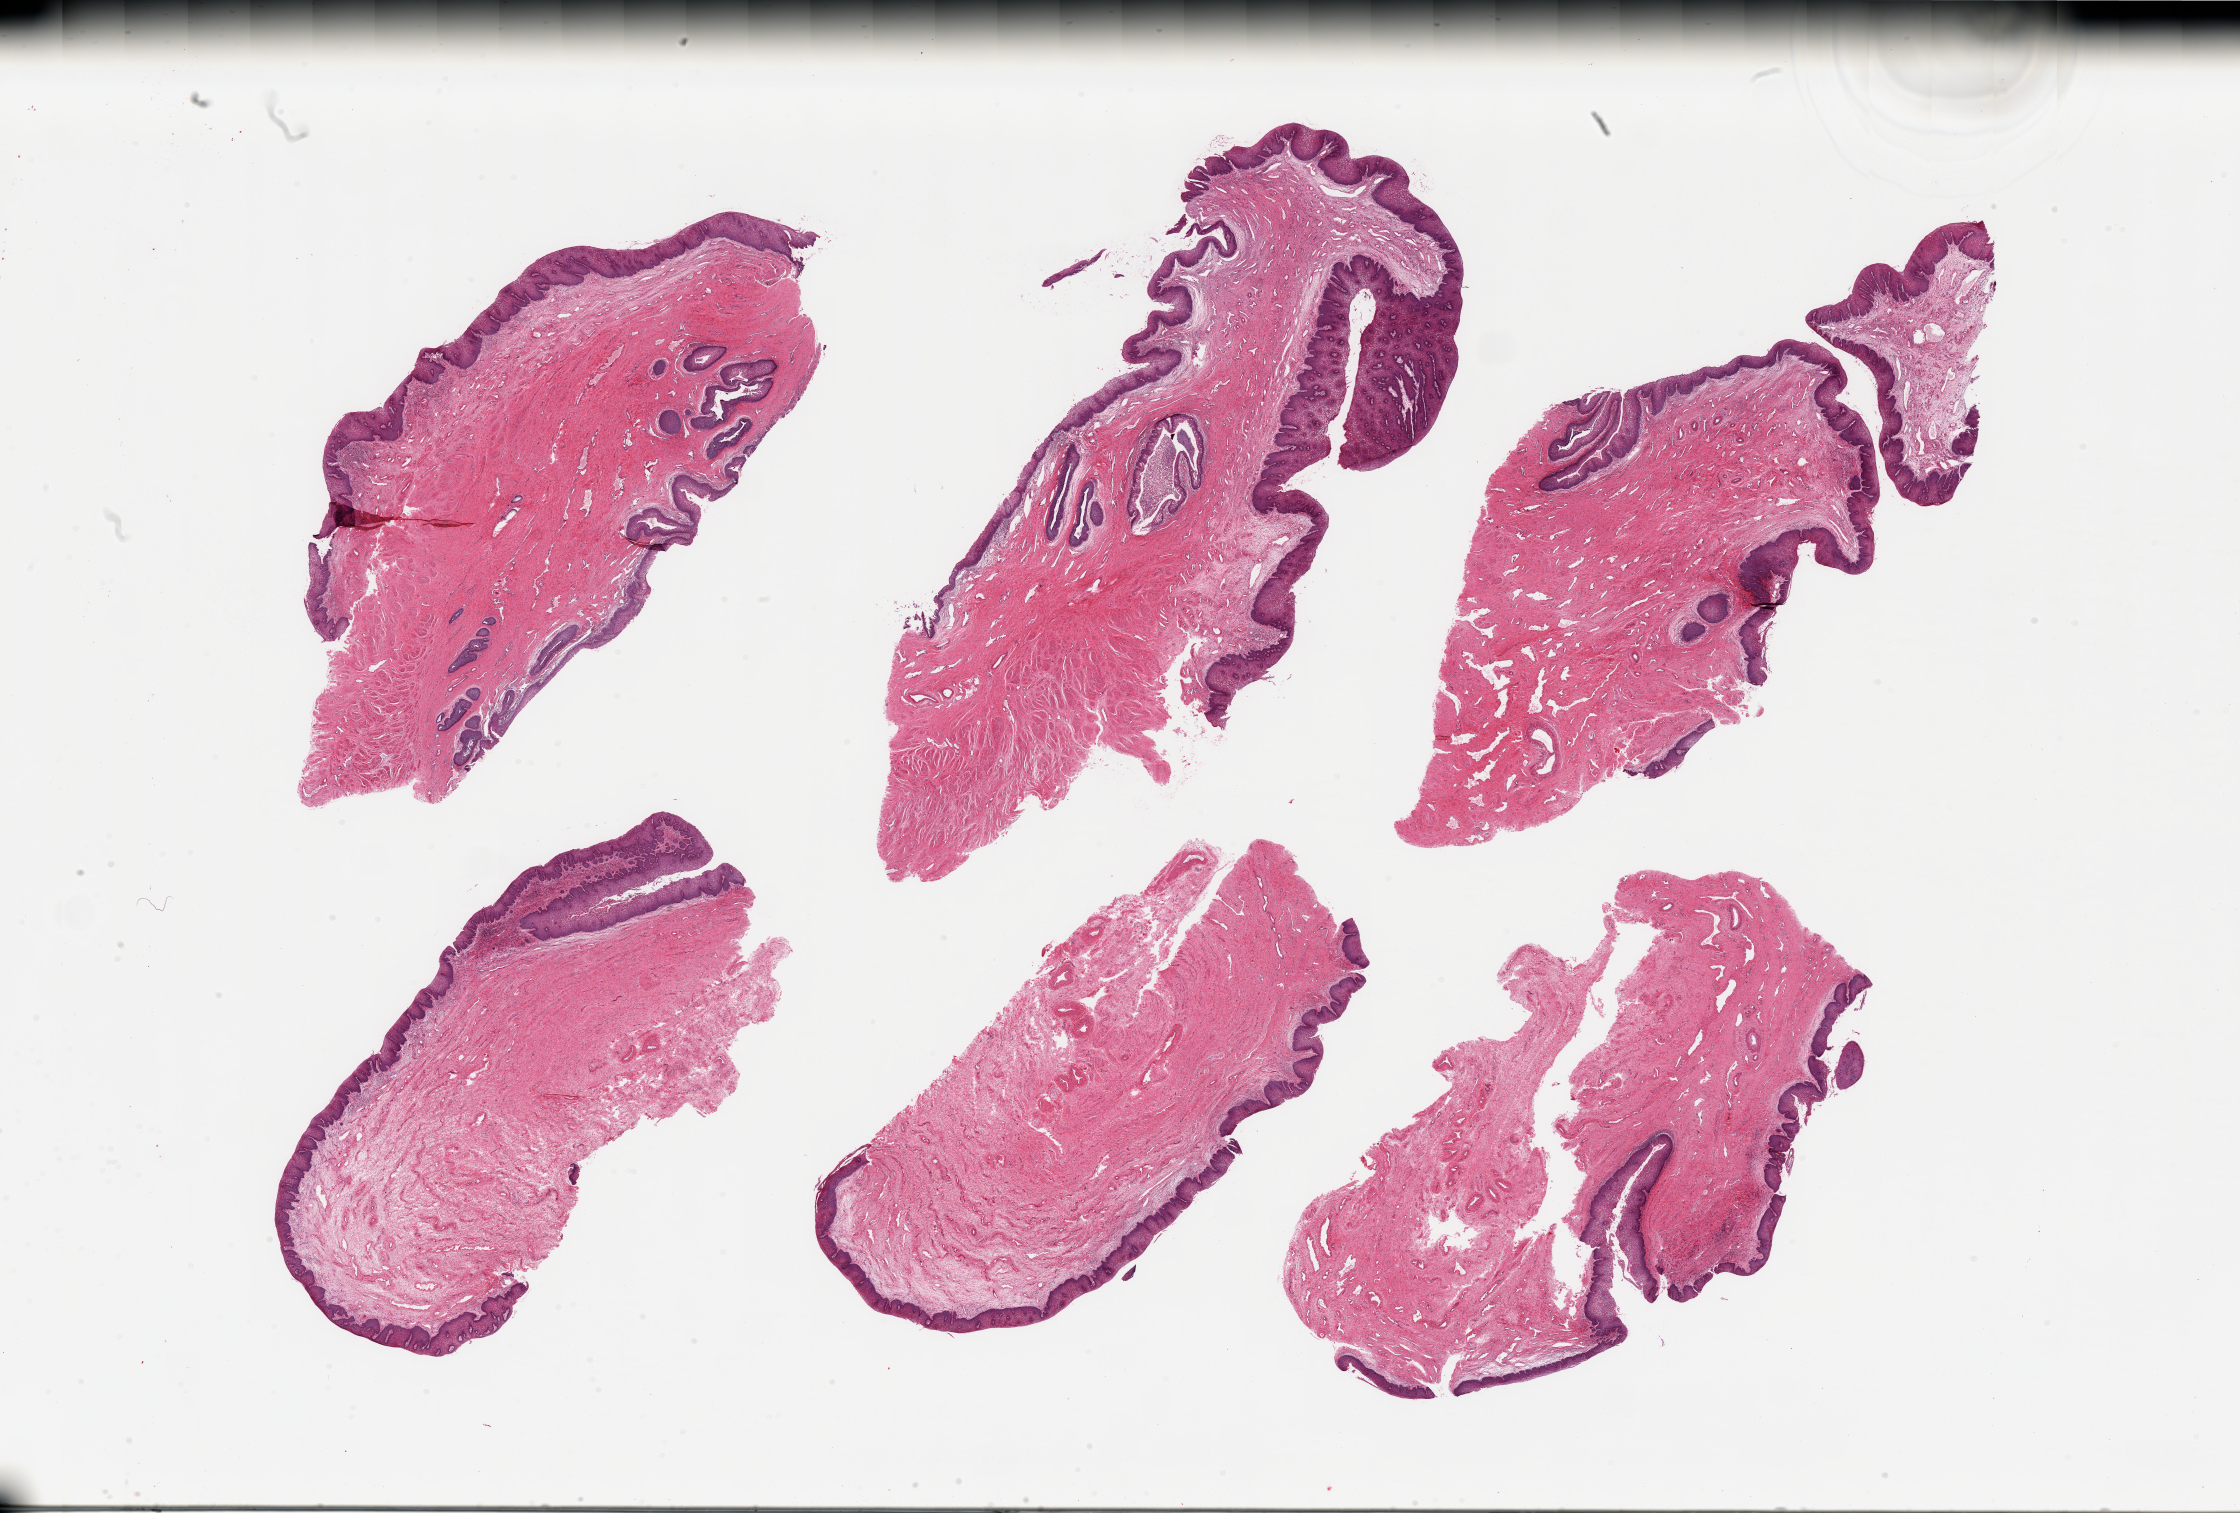
Haematoxylin and eosin whole-slide image — a low-resolution overview of the entire scanned area, about 35.4 x 23.9 mm (from a 20x scan). PAXgene-fixed paraffin-embedded (PFPE) section. Target tissue: vagina. Donor tissue sample.
Reviewer comment on this tissue sample: 6 pieces, squamous mucosa up to ~0.4mm, submucosal Mullerian rests with squamous metaplasia present.